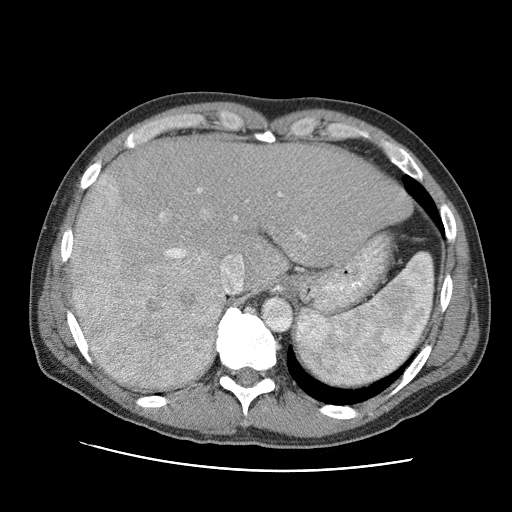
Contrast-enhanced abdominal CT (liver protocol), one axial slice. Slice 71 of 95 in the series (ordered by position). Reconstruction kernel STANDARD. One of 2 acquisitions stored at this slice position. Soft-tissue window (W 400 / L 40 HU). 2.5 mm slice thickness. 512 × 512 image matrix, field of view 360 × 360 mm. From the clinical record (not read from this slice): diagnosis: hepatocellular carcinoma (patient treated with transarterial chemoembolisation; whether this scan precedes or follows treatment is not stated here); TNM stage (as recorded): Stage-IVA.
Annotated regions visible in this slice (semi-automatic segmentation, software-assisted and operator-edited):
- liver parenchyma outside the tumour (the mass and vessels are separate outlines, so this box may not span the whole liver): box from (x=72, y=136) to (x=412, y=364) px
- mass: (x=66, y=174)–(x=224, y=393)
- liver vessels: (x=159, y=187)–(x=306, y=294)